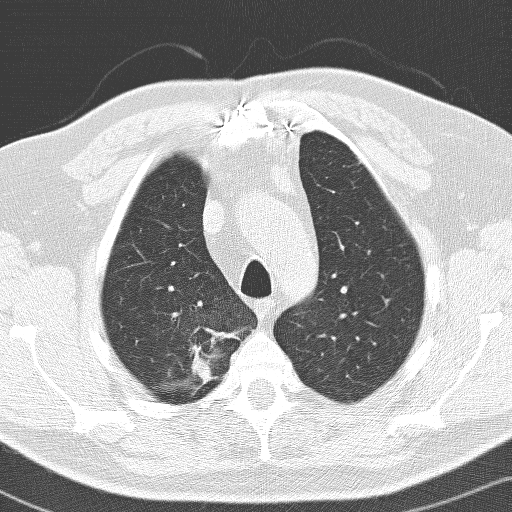
Axial slice from a low-dose chest CT screening exam; first (baseline) screen; lung window (W 1500 / L -600 HU); 3.2 mm slice thickness; slice 26 of 141 in the series; 512 × 512 image matrix, field of view 326 × 326 mm. Male participant, aged 66 years at enrolment.
• Expert-annotated lung lesion, bounding box (x1, y1, x2, y2) in pixels: (155, 317, 231, 394).
• The exam's reader record, not a measurement of the box and not confirmed to be the same lesion: non-calcified nodule or mass ≥4 mm, right upper lobe, 36 × 30 mm, spiculated (stellate) margins, soft tissue attenuation.
• Official screen result: positive, change unspecified: nodule(s) >= 4 mm or enlarging nodule(s), mass(es), or other non-specific abnormalities suspicious for lung cancer.
• Lung cancer was diagnosed 103 days after this screen: adenocarcinoma, NOS, right upper lobe, poorly differentiated (G3), stage IIB (AJCC 6th edition), 33 mm at pathology.